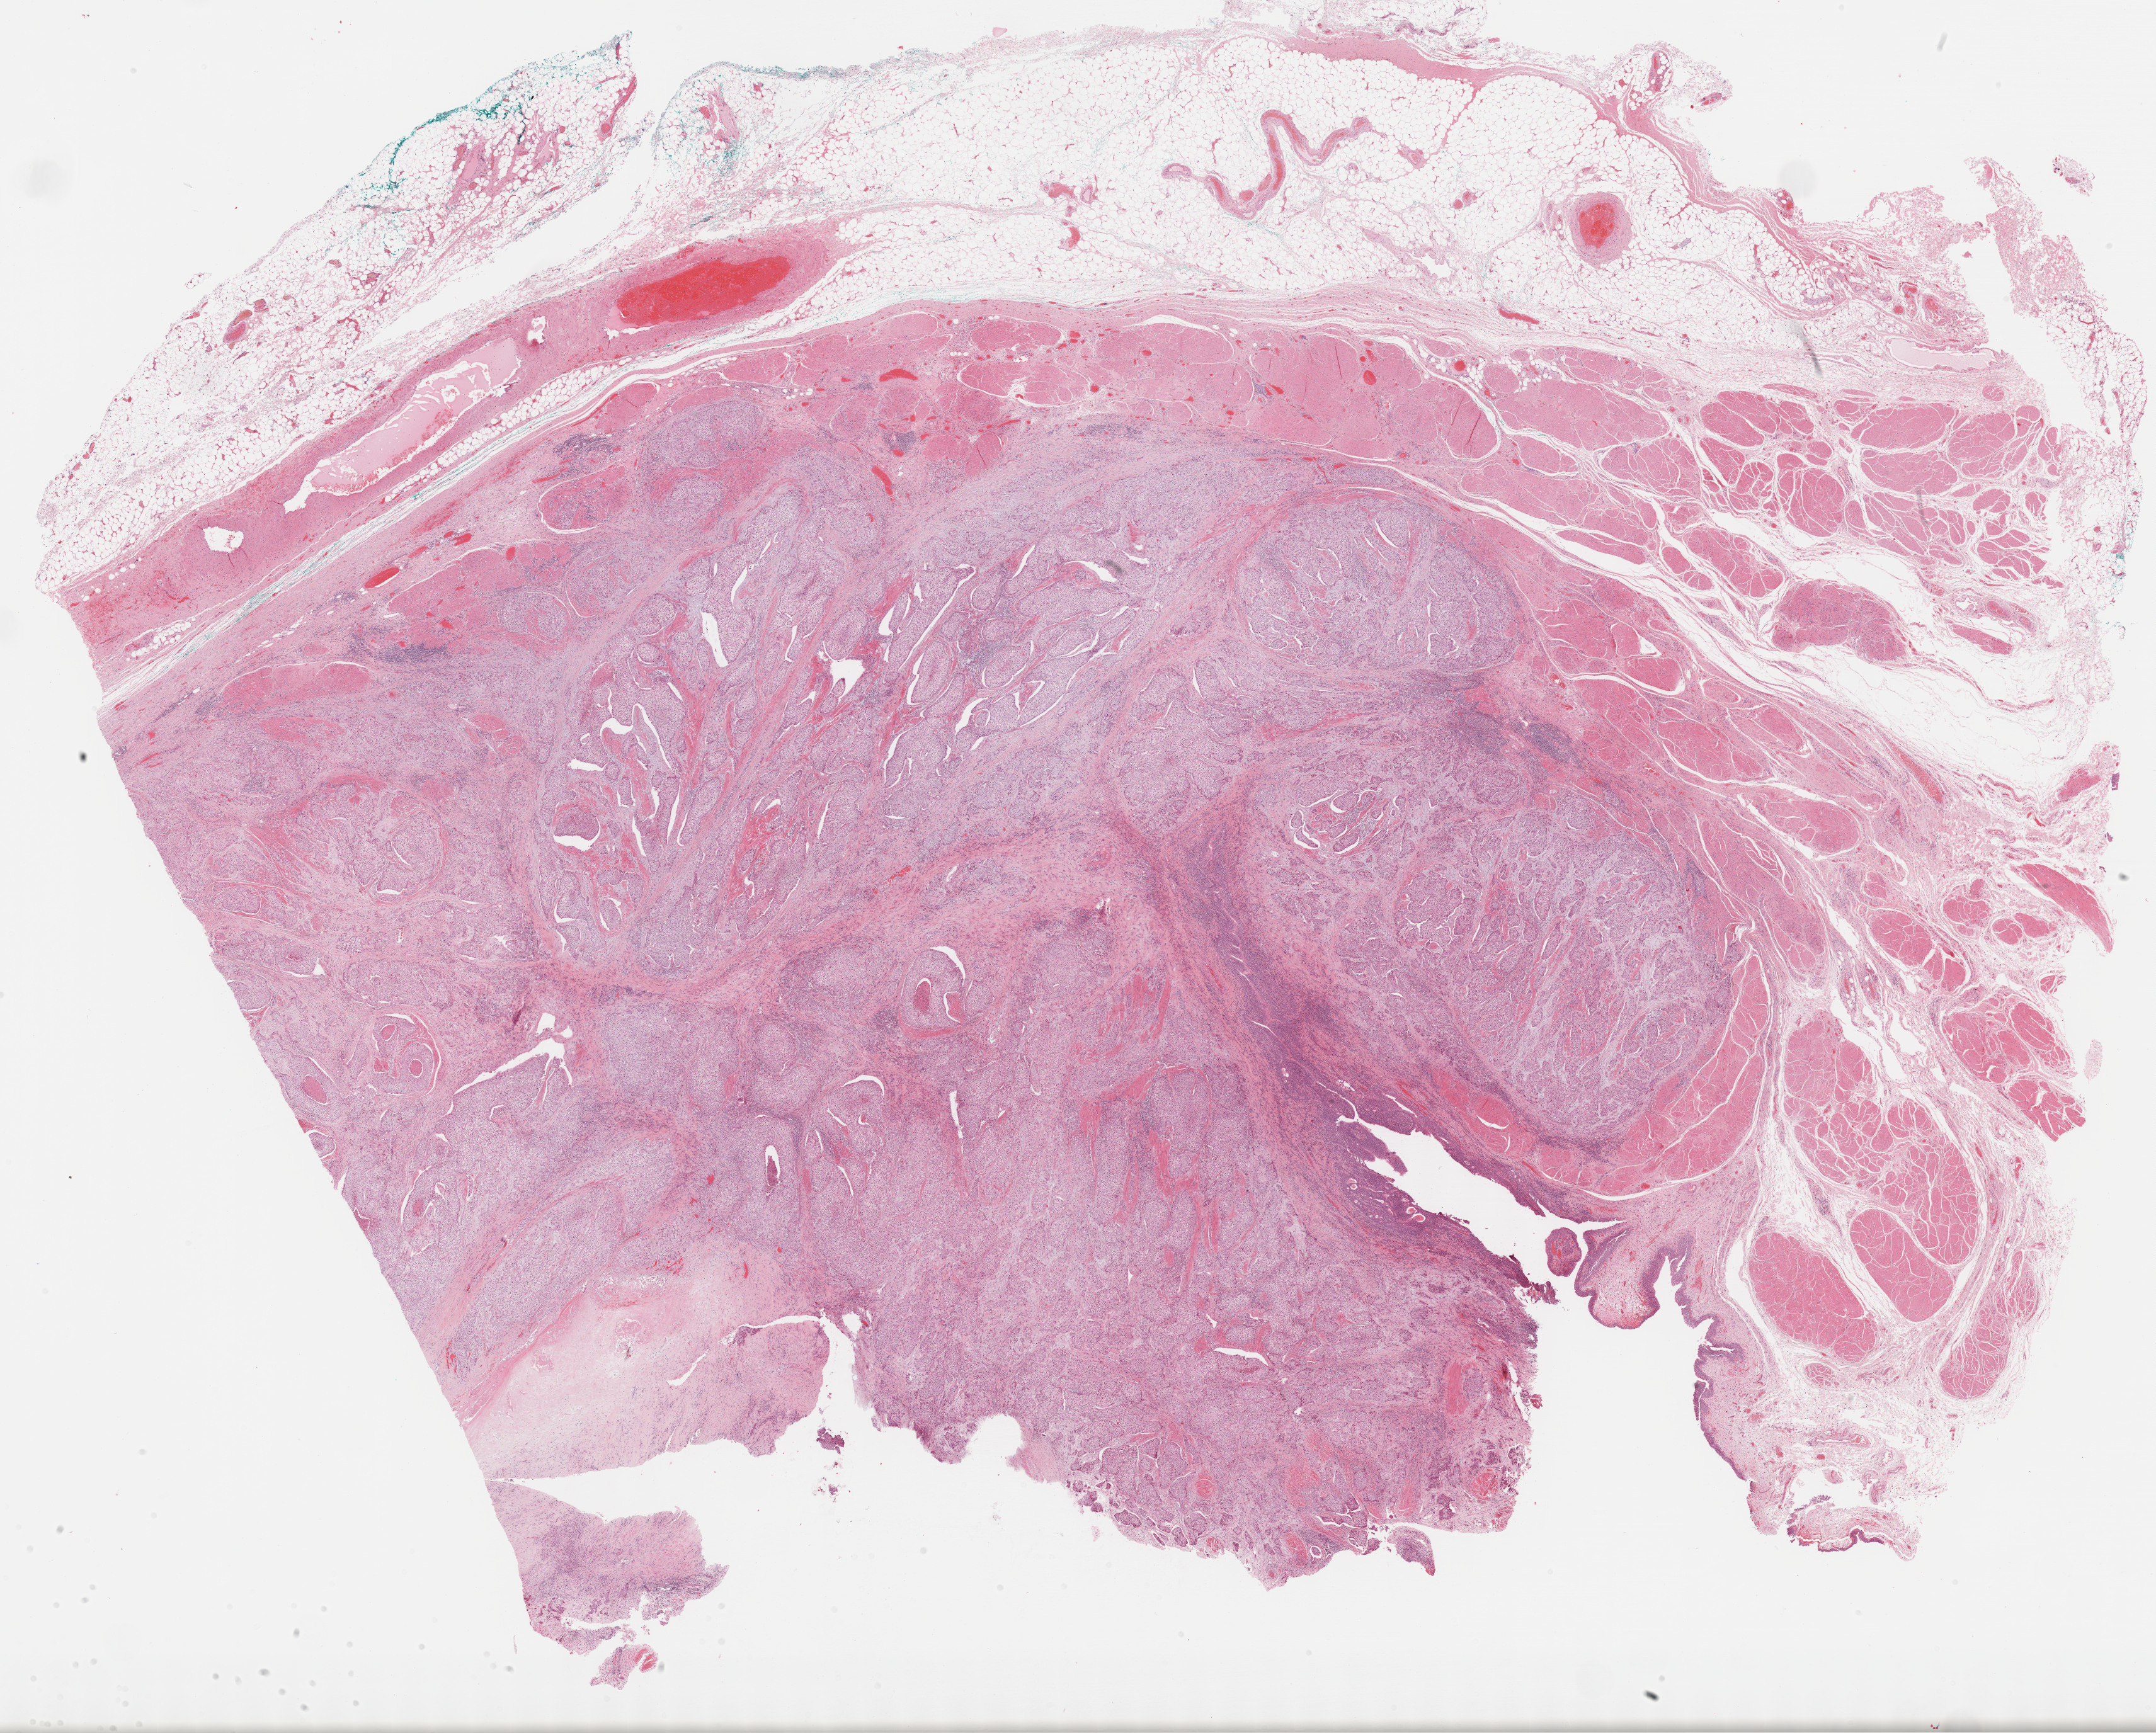
H&E-stained whole-slide image, shown as a low-resolution overview of the whole scanned area (about 27.7 x 22.3 mm, acquisition: 40x scan), formalin-fixed paraffin-embedded (FFPE) diagnostic section, sample: primary tumour, bladder. Male patient; age at initial diagnosis 82 years. Histologic grade: high grade.
AJCC pathologic stage: III (7th edition). Diagnosis: Transitional cell carcinoma (posterior wall of bladder).